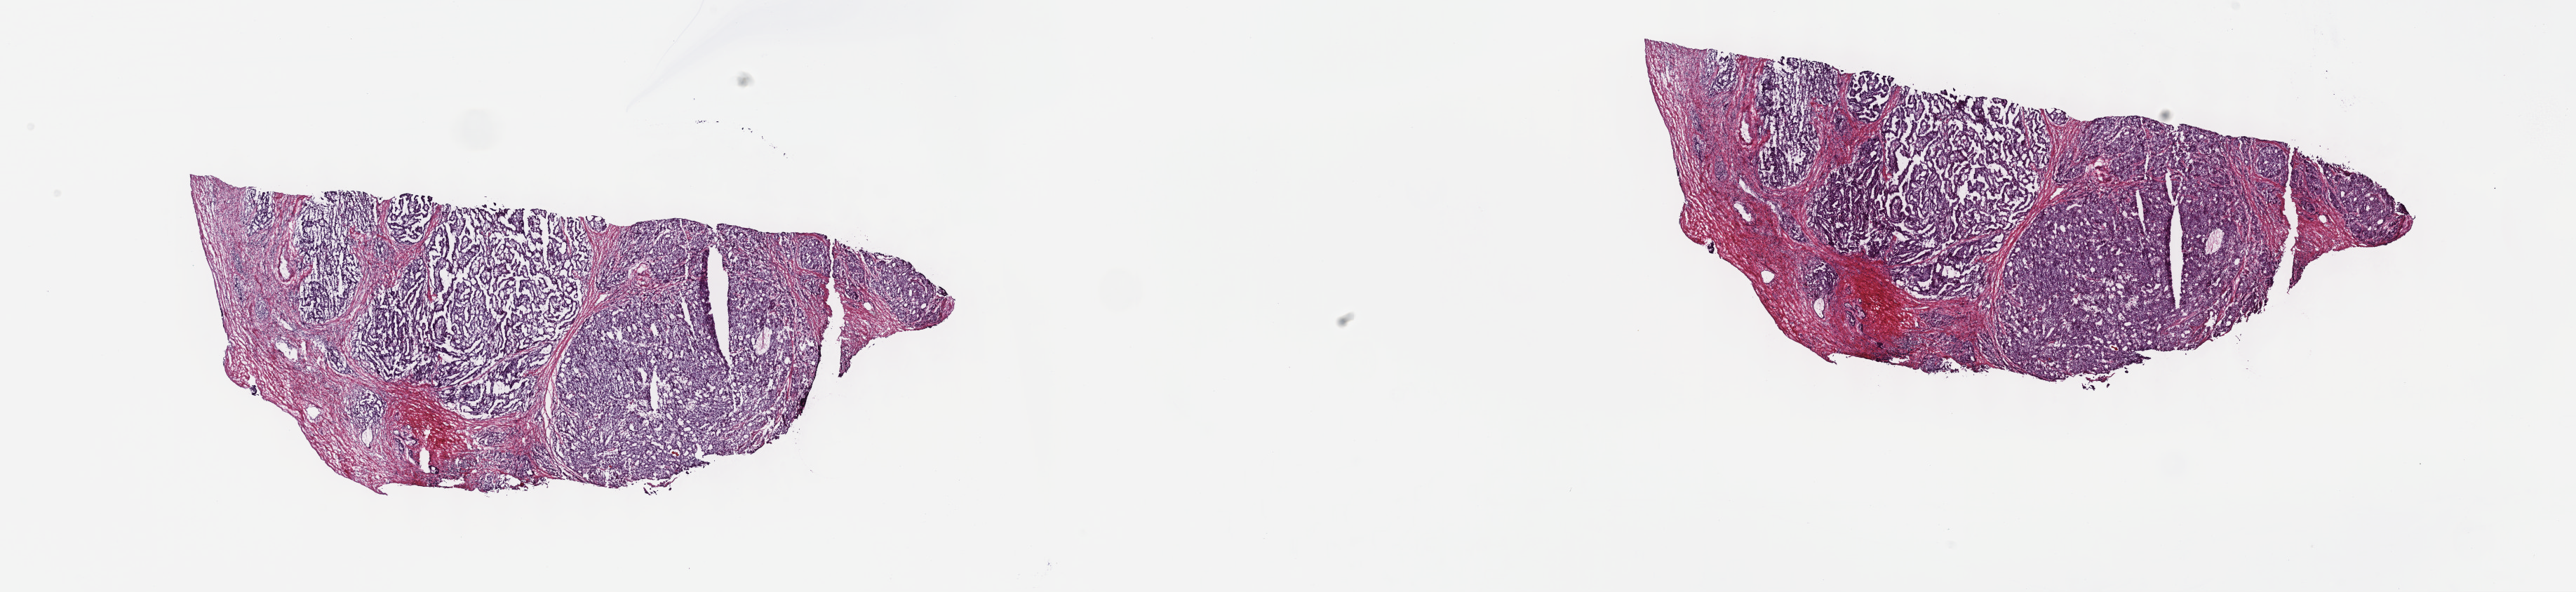
Digitized Hematoxylin and eosin (H&E) stained tissue section (whole slide), shown as a low-resolution overview of the whole scanned area (about 29.7 x 6.8 mm, acquisition: 40x scan); frozen section from the top of the tissue portion; prostate, primary tumour sample. Male patient; age at initial diagnosis 66 years. Gleason score: 9 (4+5). Slide review estimates, as recorded: tumour cells 80%, tumour nuclei 80%, normal cells 0%, stromal cells 20%, necrosis 0%. Infiltration values recorded for this section: lymphocyte infiltration 2%, monocyte infiltration 1%, neutrophil infiltration 1%.
Laterality: bilateral. Lymph nodes positive (case pathology): 0 of 10 examined. Pathologic diagnosis: Adenocarcinoma, NOS (prostate gland).